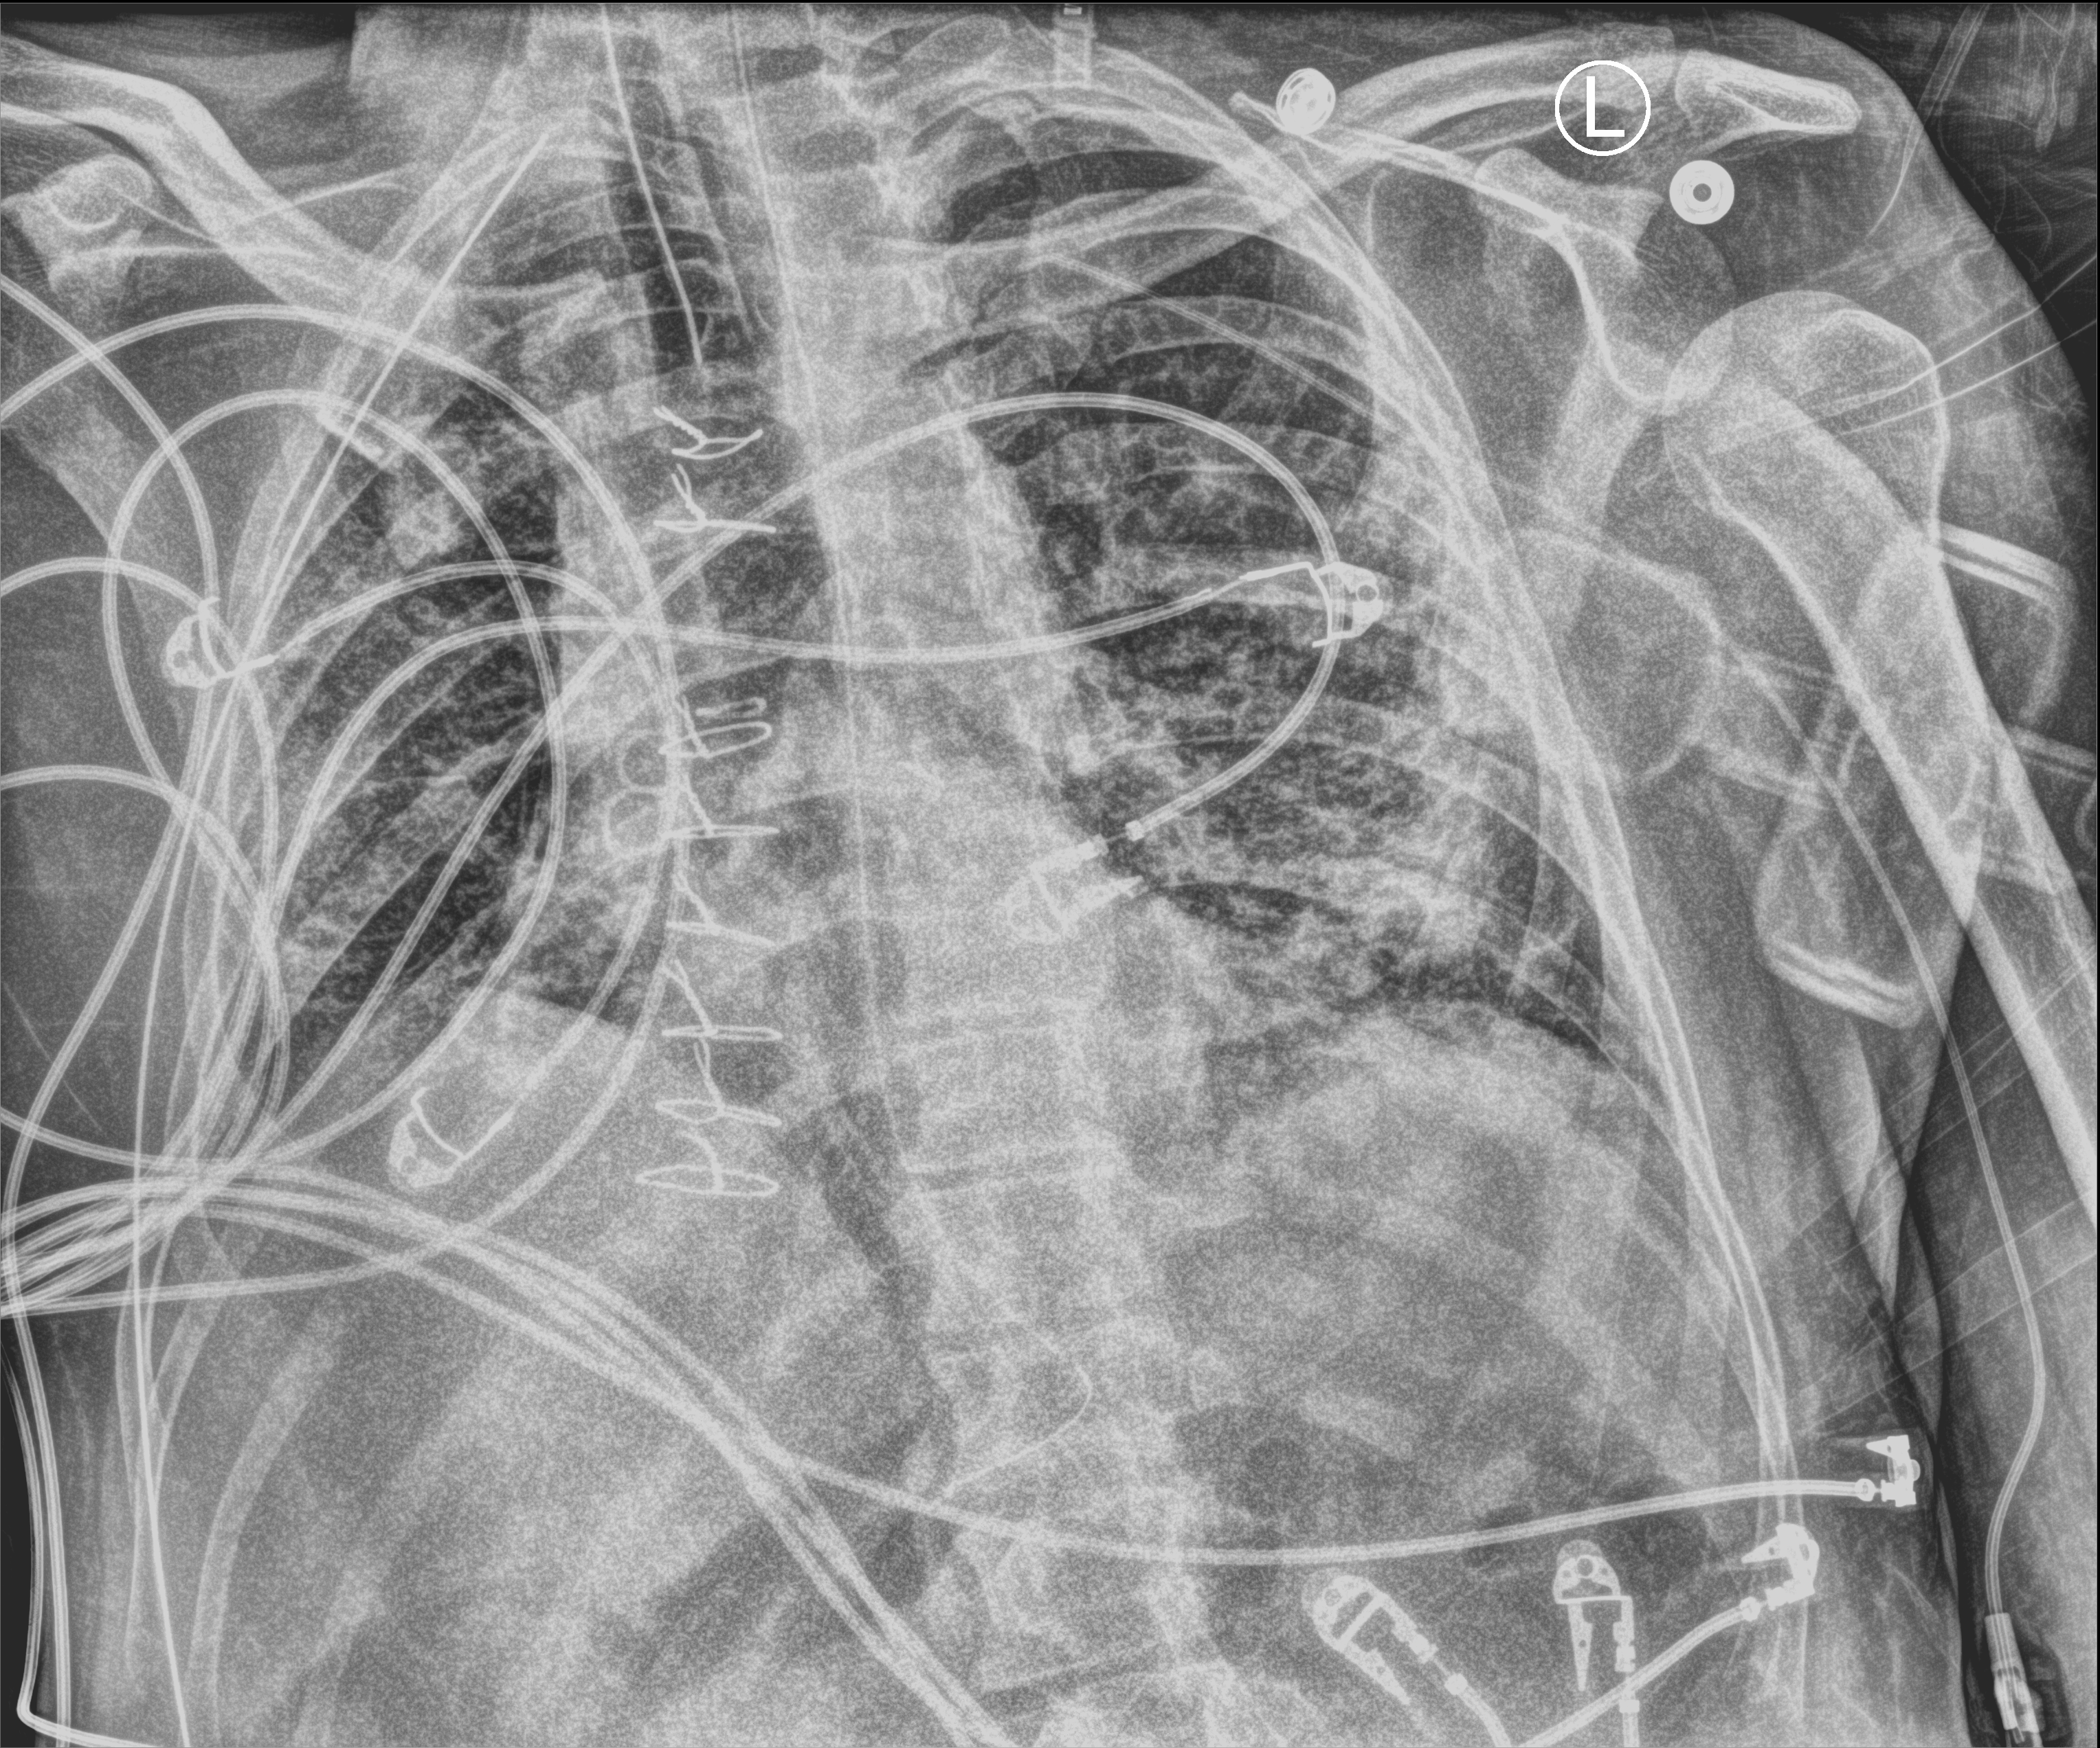
Chest X-ray (portable). Male patient hospitalised with COVID-19, age 18–59 years.
Admission-level facts for this patient (not findings on this image; timing relative to this image not recorded): smoking status (admission record): former; mechanically ventilated during this hospital stay: yes.